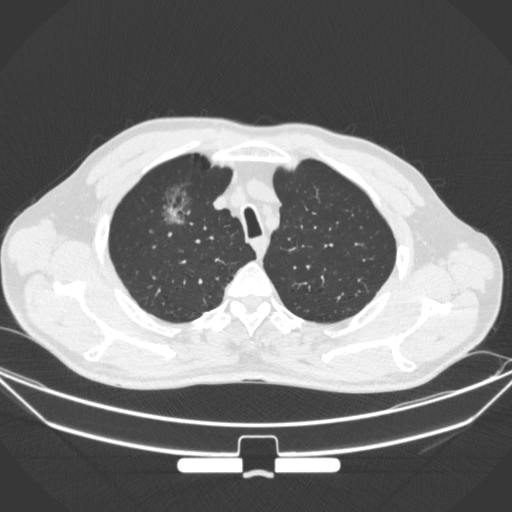
Chest CT, one axial slice; slice 285 of 355 in the series (ordered by position); 120 kVp; lung window (W 1500 / L -600 HU); 1 mm slice thickness; 512 × 512 image matrix, field of view 399 × 399 mm. Male patient, age 67 years. Case-level facts recorded for this patient, not image findings: clinical TNM (as recorded): T1c N0 M0.
Structures marked on this image (rectangle marked by the reading radiologist):
- lung tumour (recorded histology: adenocarcinoma): bounding box [x1, y1, x2, y2] px = [149, 174, 204, 233]